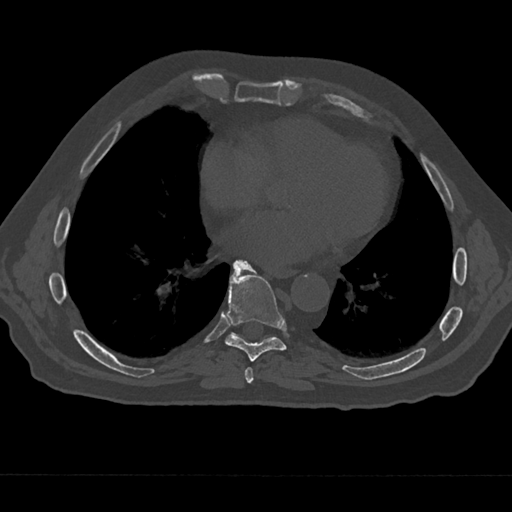
CT including the spine, one axial slice. Position 308 of 797 along the scan axis. 120 kVp. Bone window (W 1800 / L 400 HU). 0.5 mm slice thickness. 512 × 512 image matrix. Male patient, age 75 years. From the clinical record (not read from this slice): primary cancer: renal; vertebrae with lytic lesions (as recorded): T4.
Structures marked on this image (semi-automatic segmentation, software-assisted and operator-edited):
- T7 vertebra: bounding box <238,367,259,384> (left, top, right, bottom; pixels)
- T8 vertebra: <225,260,287,362>